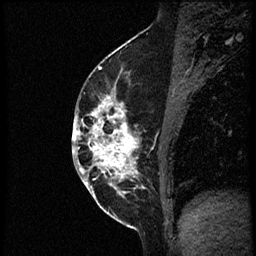
Breast MRI (dynamic contrast-enhanced), one sagittal slice. Slice 30 of 56 in the series (ordered by position). Dynamic contrast-enhanced study with each time point stored as its own series, time point 2 of 3 at this slice position (early post-contrast, ordered by acquisition time). 1.5 T. TE 4.2 ms, TR 21.3 ms. 2 mm slice thickness. 256 × 256 image matrix, field of view 200 × 200 mm. Female patient, age 41 years. From the clinical record (not read from this slice): setting: breast cancer imaged before/during neoadjuvant chemotherapy; receptor status: HER2-positive.
Structures marked on this image (semi-automatically segmented with operator editing):
- analysis volume of interest (the breast-tissue region the enhancement analysis was run in; not a lesion): bounding box <86,73,177,205> (left, top, right, bottom; pixels)
- tumour enhancement mask (voxels above the 100 % enhancement threshold inside the analysis volume of interest): <86,83,144,196>